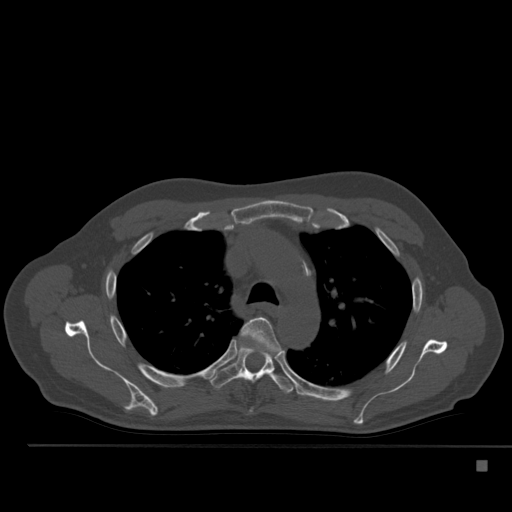
CT including the spine, one axial slice; position 372 of 517 along the scan axis; reconstruction kernel Br40s; 120 kVp; bone window (W 1800 / L 400 HU); 1.5 mm slice thickness; 512 × 512 image matrix, field of view 408 × 408 mm. Patient: male, 70 years. From the clinical record (not read from this slice): primary cancer: renal.
Annotated regions visible in this slice (semi-automatically segmented with operator editing):
- T4 vertebra: bounding box [x1, y1, x2, y2] px = [240, 316, 280, 354]
- T5 vertebra: [211, 340, 296, 394]